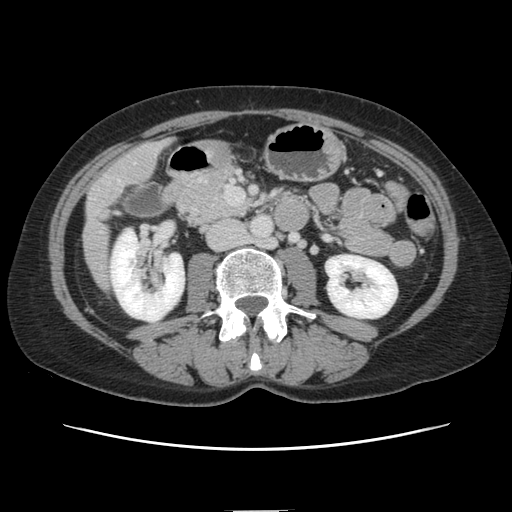
Contrast-enhanced abdominal CT, one axial slice; 120 kVp; intravenous contrast given; soft-tissue window (W 400 / L 40 HU); 2.5 mm slice thickness; 512 × 512 image matrix, field of view 350 × 350 mm. Female patient, age 63 years. From the clinical record (not read from this slice): diagnosis: colorectal cancer liver metastases, imaged before liver resection; multiple liver metastases: yes; largest metastasis: 3.2 cm; disease in both lobes: yes.
Outlined on this slice (expert manual segmentation):
- liver: bounding box <84,142,165,287> (left, top, right, bottom; pixels)